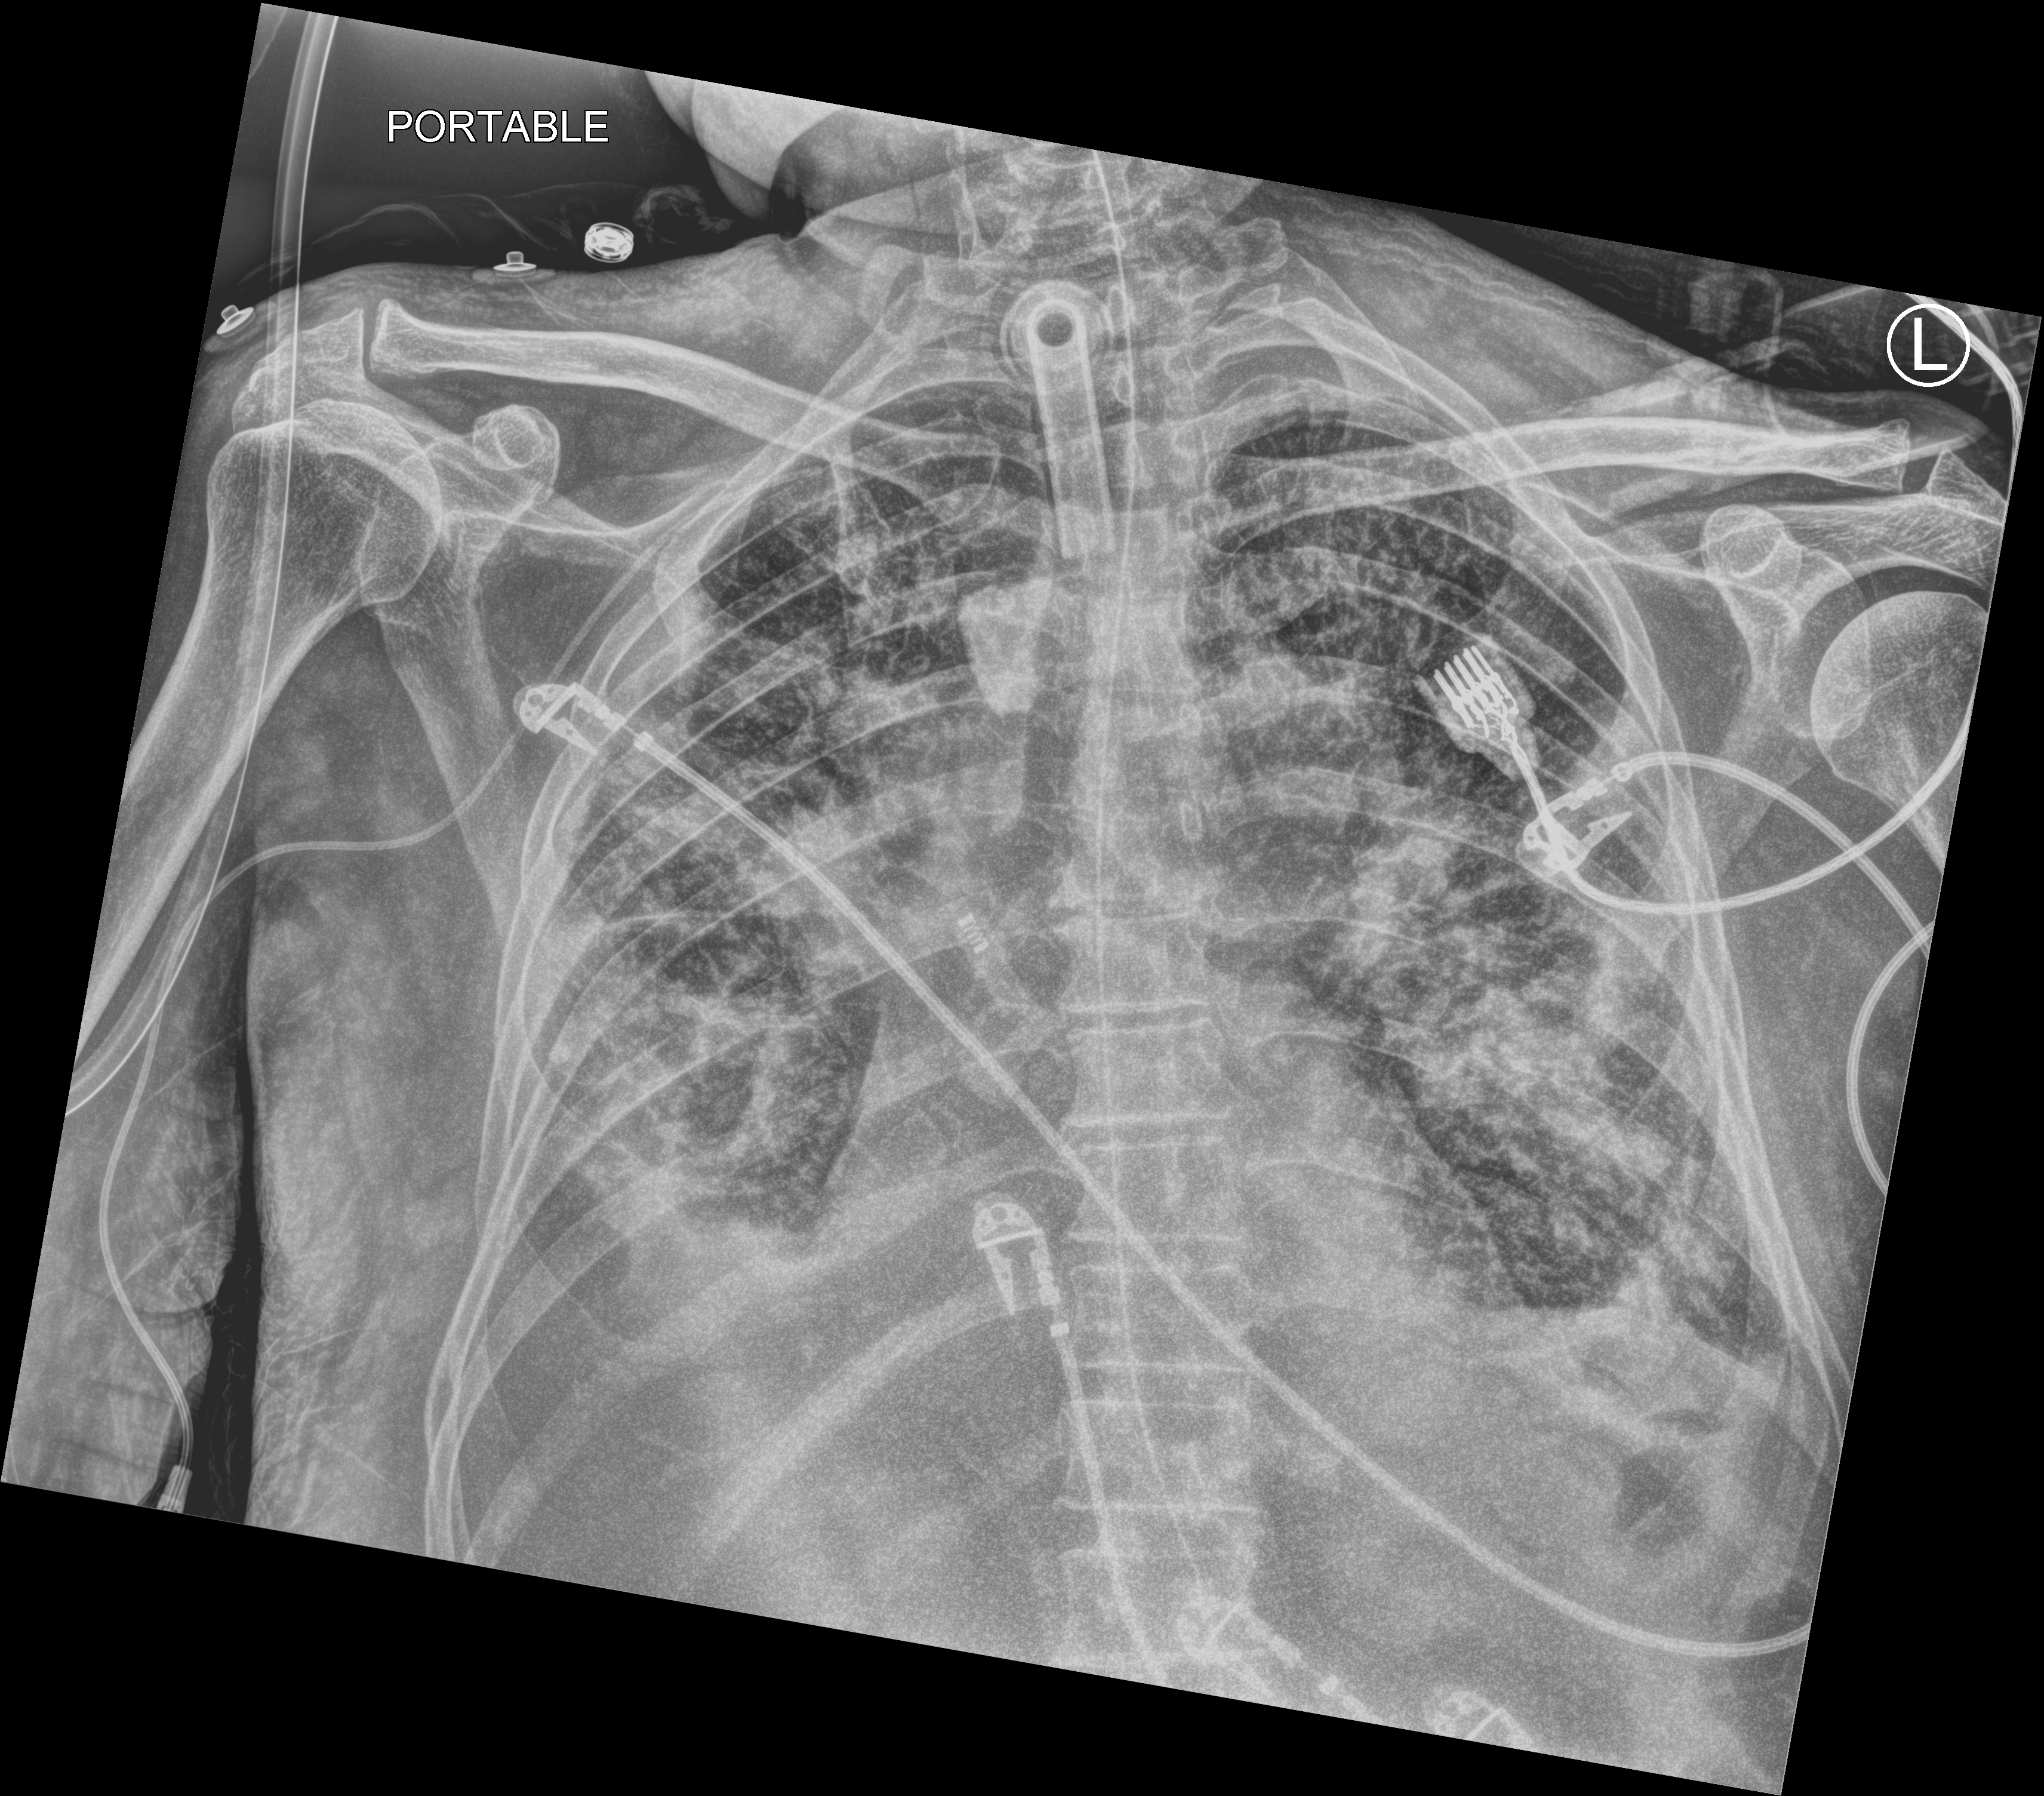
Bedside chest radiograph (computed radiography); anteroposterior (AP) projection. Male patient hospitalised with COVID-19, age 75–90 years.
From the hospital-stay record, not from the radiograph (when in the stay this image was taken is not recorded): admitted to intensive care during this hospital stay: yes; mechanically ventilated during this hospital stay: yes.